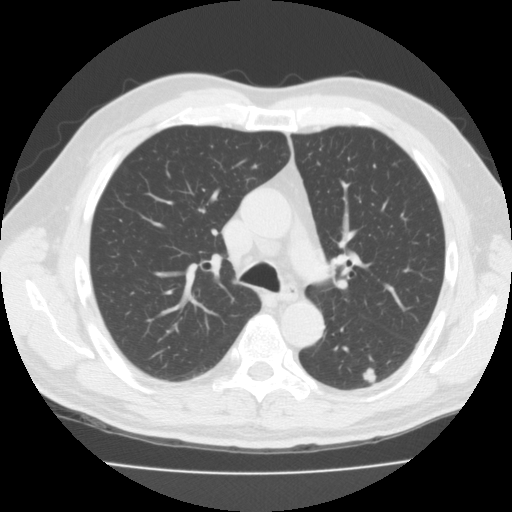
Low-dose screening chest CT, one axial slice; position 66 of 99 along the scan axis; reconstruction kernel FC02; lung window (W 1500 / L -600 HU); 3 mm slice thickness; 512 × 512 image matrix, field of view 359 × 359 mm.
Structures marked on this image (outlined manually by an expert reader):
- lesion 1 (tumor, lower lobe of left lung): bounding box [x1, y1, x2, y2] px = [363, 368, 376, 383]